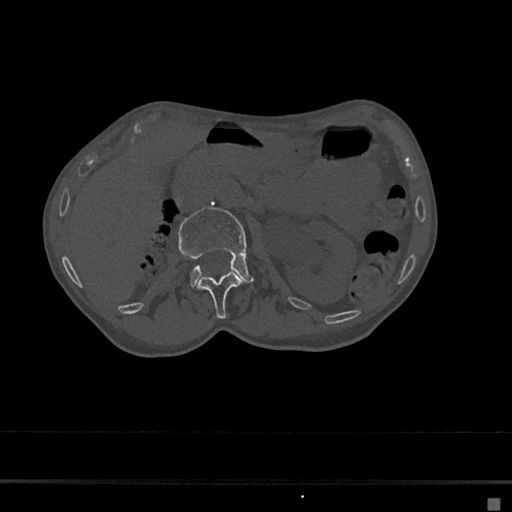
CT including the spine, one axial slice. Slice 43 of 797 in the series (ordered by position). Bone window (W 1800 / L 400 HU). 0.5 mm slice thickness. 512 × 512 image matrix, field of view 360 × 360 mm. Patient: female, 68 years. From the clinical record (not read from this slice): primary cancer: renal.
Structures marked on this image (semi-automatic segmentation, software-assisted and operator-edited):
- L1 vertebra: box from (x=197, y=272) to (x=241, y=319) px
- L2 vertebra: (x=178, y=207)–(x=252, y=287)